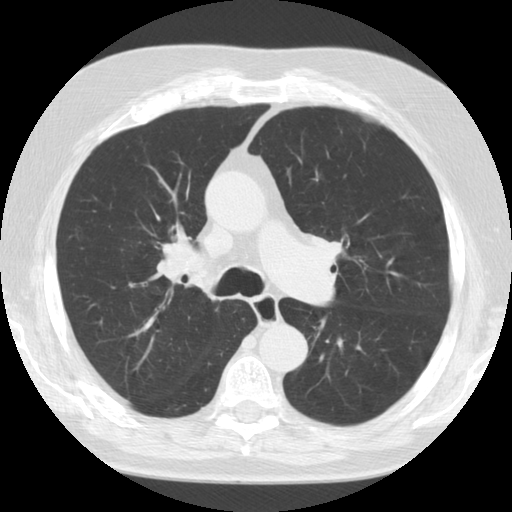
Low-dose screening chest CT, axial slice. Baseline annual screen. Lung window (W 1500 / L -600 HU). Standard (soft-tissue) reconstruction kernel (STANDARD). 120 kVp. Male participant, aged 72 years at enrolment. Former smoker at enrolment.
• Expert reader's lesion annotation, bounding box [x1, y1, x2, y2] px = [137, 227, 215, 296].
• No non-calcified nodule or mass ≥4 mm was recorded by the screening reader at this exam.
• Participant outcome: lung cancer diagnosed 779 days after this screen (after the third annual screen) — small cell carcinoma, NOS, right upper lobe, stage IV (AJCC 6th edition), 7 mm at pathology.